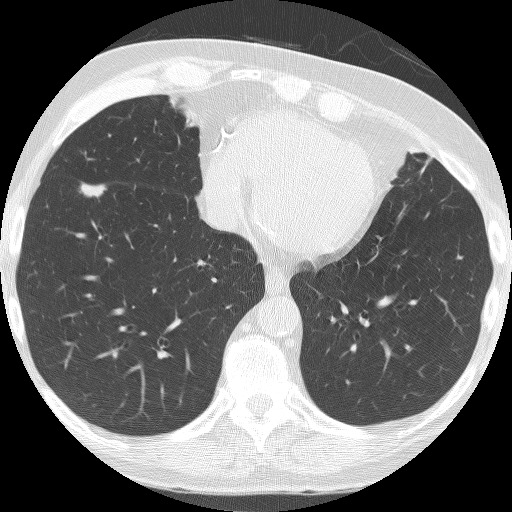
Axial slice from a low-dose chest CT screening exam, baseline screening round, lung window (W 1500 / L -600 HU), 2.5 mm slice thickness, lung (sharp) reconstruction kernel (BONE), 120 kVp, 512 × 512 image matrix, field of view 320 × 320 mm. Male participant, aged 74 years at enrolment. Former smoker at enrolment.
Lesion marked by an expert reader, bounding box <72,171,118,208> (left, top, right, bottom; pixels). The screening reader recorded 4 non-calcified nodules or masses ≥4 mm on this exam (right lower lobe, right lower lobe, right lower lobe, right lower lobe); which of them this box marks is not recorded.